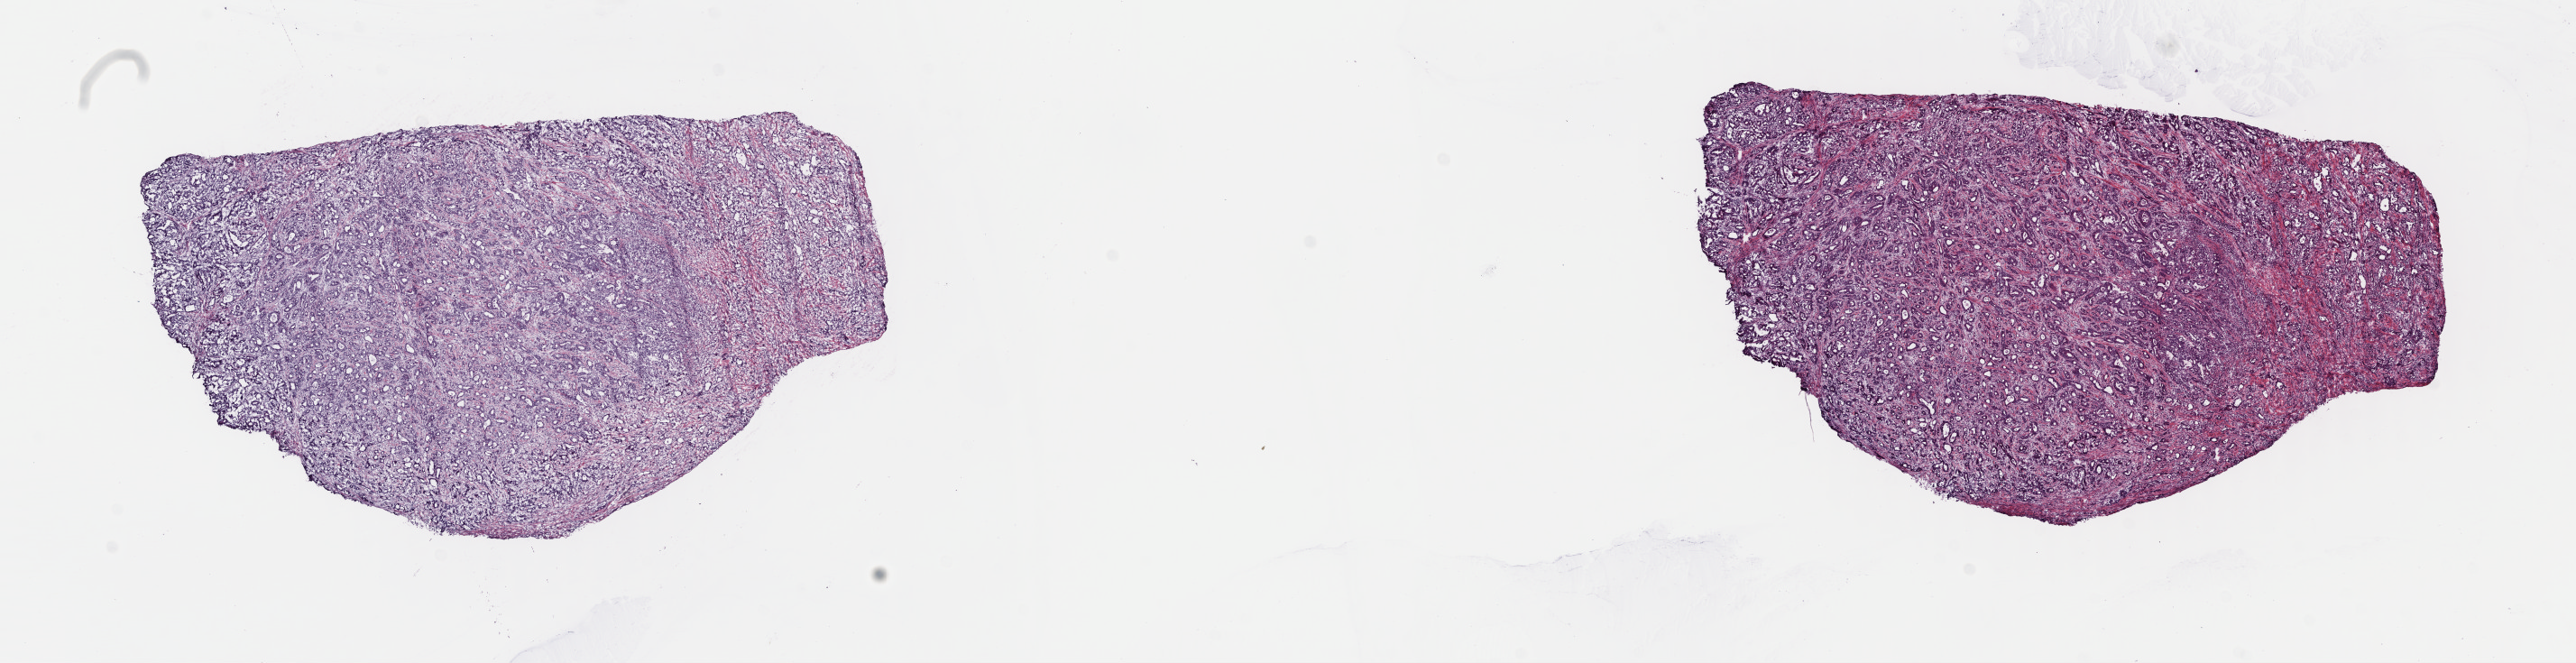
Digitized H&E tissue section (whole slide) — a low-resolution overview of the entire scanned area, about 22.4 x 5.8 mm (from a 40x scan), frozen section from the top of the tissue portion, sample: primary tumour, stomach. Patient: male, age at initial diagnosis 61 years. Composition of this section per pathologist review: tumour cells 65%, tumour nuclei 70%.
Pathologic diagnosis: Adenocarcinoma, NOS (gastric antrum).